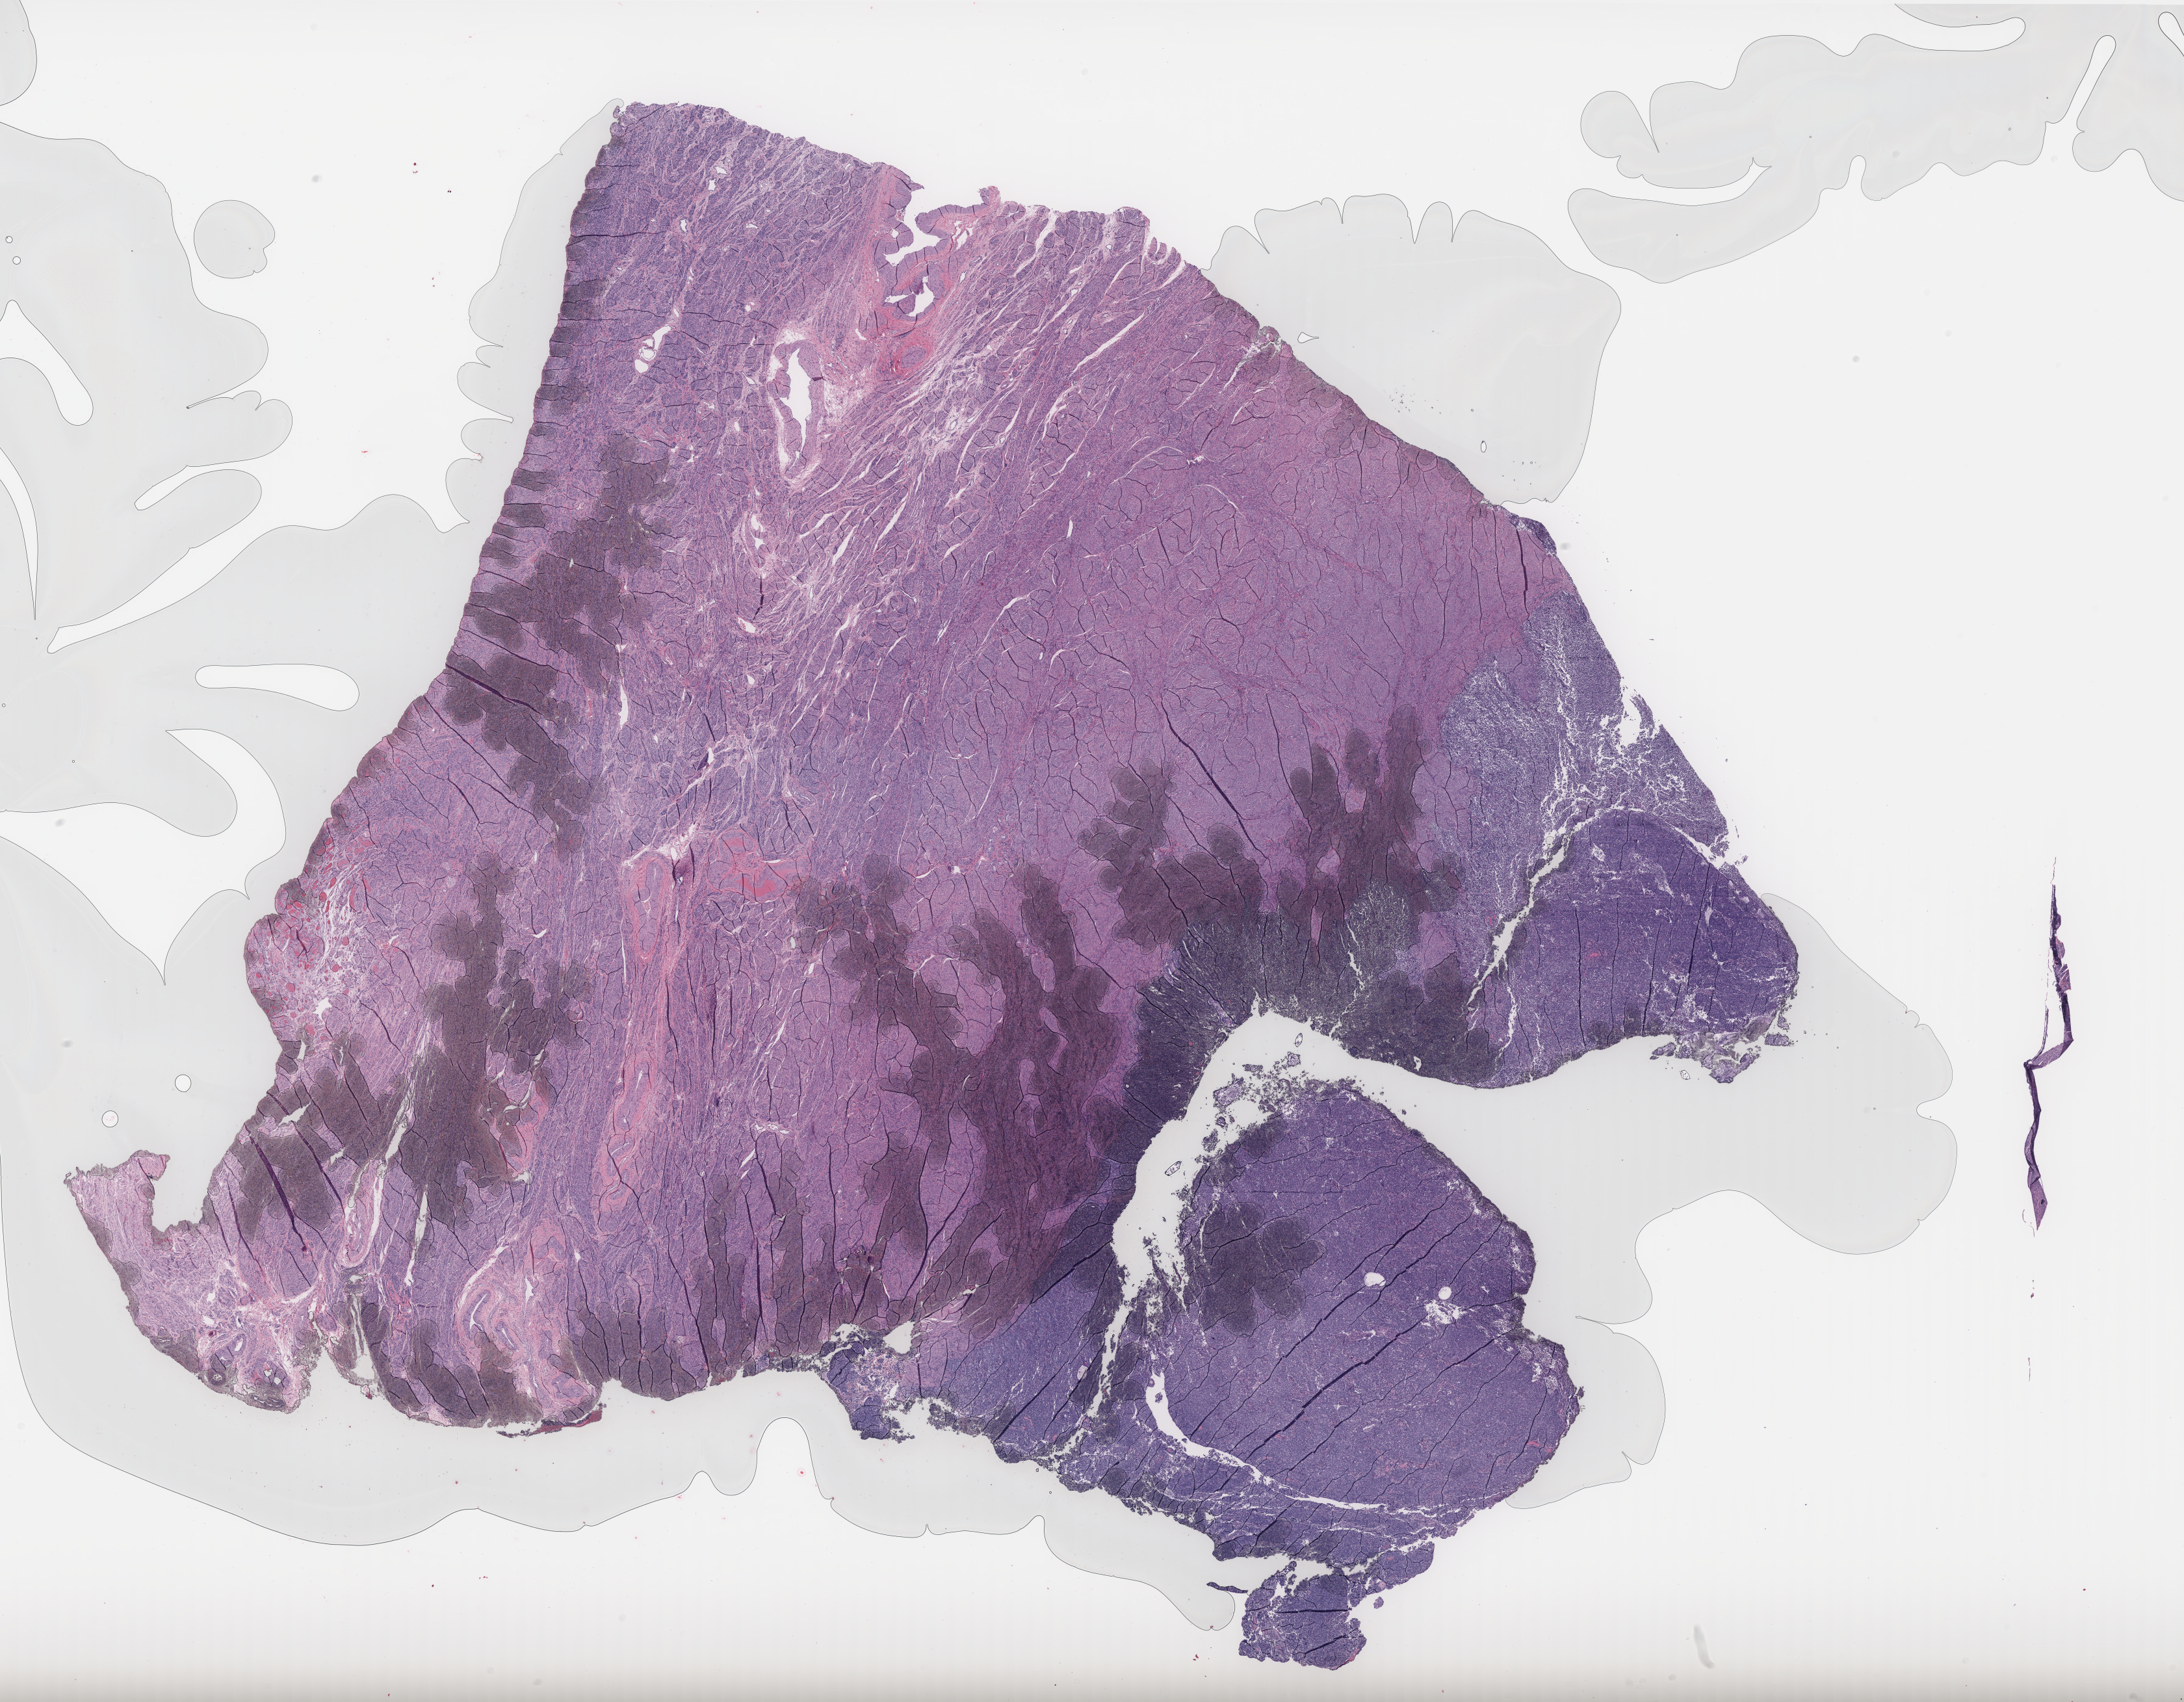
Hematoxylin and eosin (H&E) stained whole-slide image, a low-resolution overview of the entire scanned area, about 26.9 x 21.0 mm (slide scanned at 40x), formalin-fixed paraffin-embedded (FFPE) diagnostic section, sample: primary tumour, uterus. Patient: female, age at initial diagnosis 53 years. Histologic grade: G3 (poorly differentiated).
Diagnosis: Endometrioid adenocarcinoma, NOS (endometrium). FIGO stage: IIIC1.